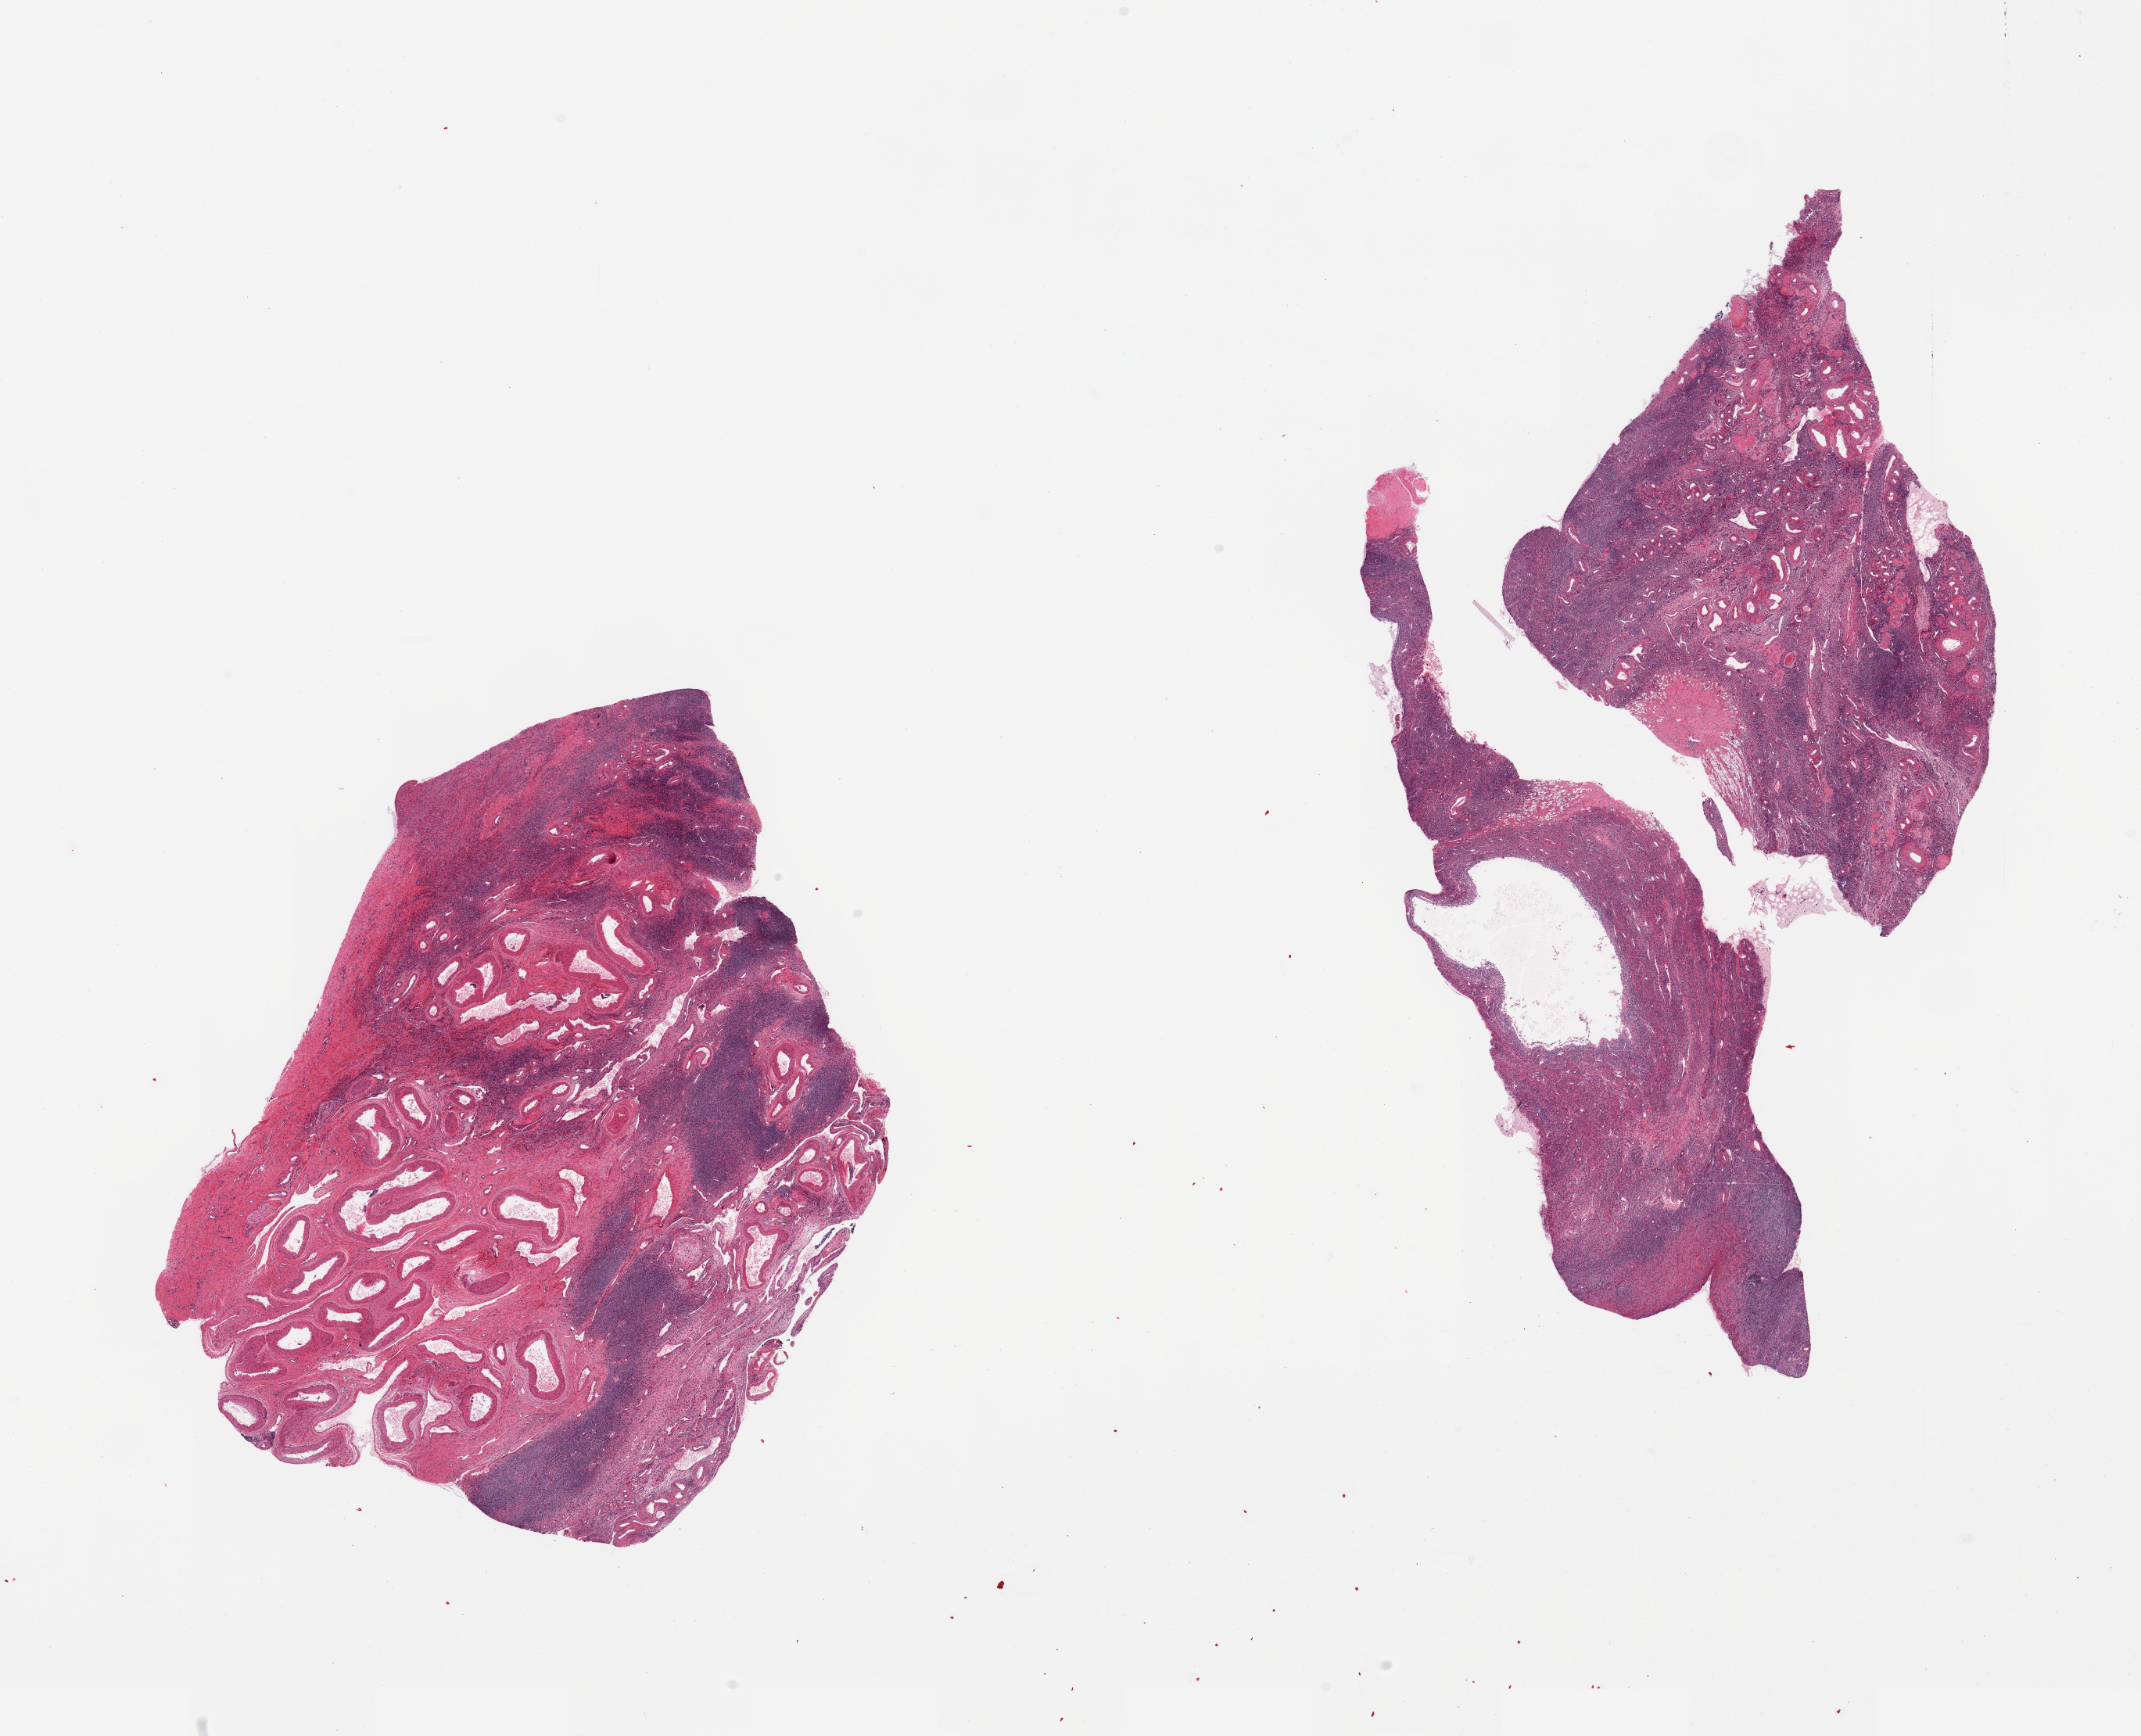
Digitized H&E-stained section — a low-resolution overview of the entire scanned area, about 21.7 x 17.6 mm, PAXgene-fixed, paraffin-embedded tissue, target tissue: ovary, donor tissue sample. Female donor.
- review note (as recorded): 2 pieces; ~80% of 1 piece is vessels